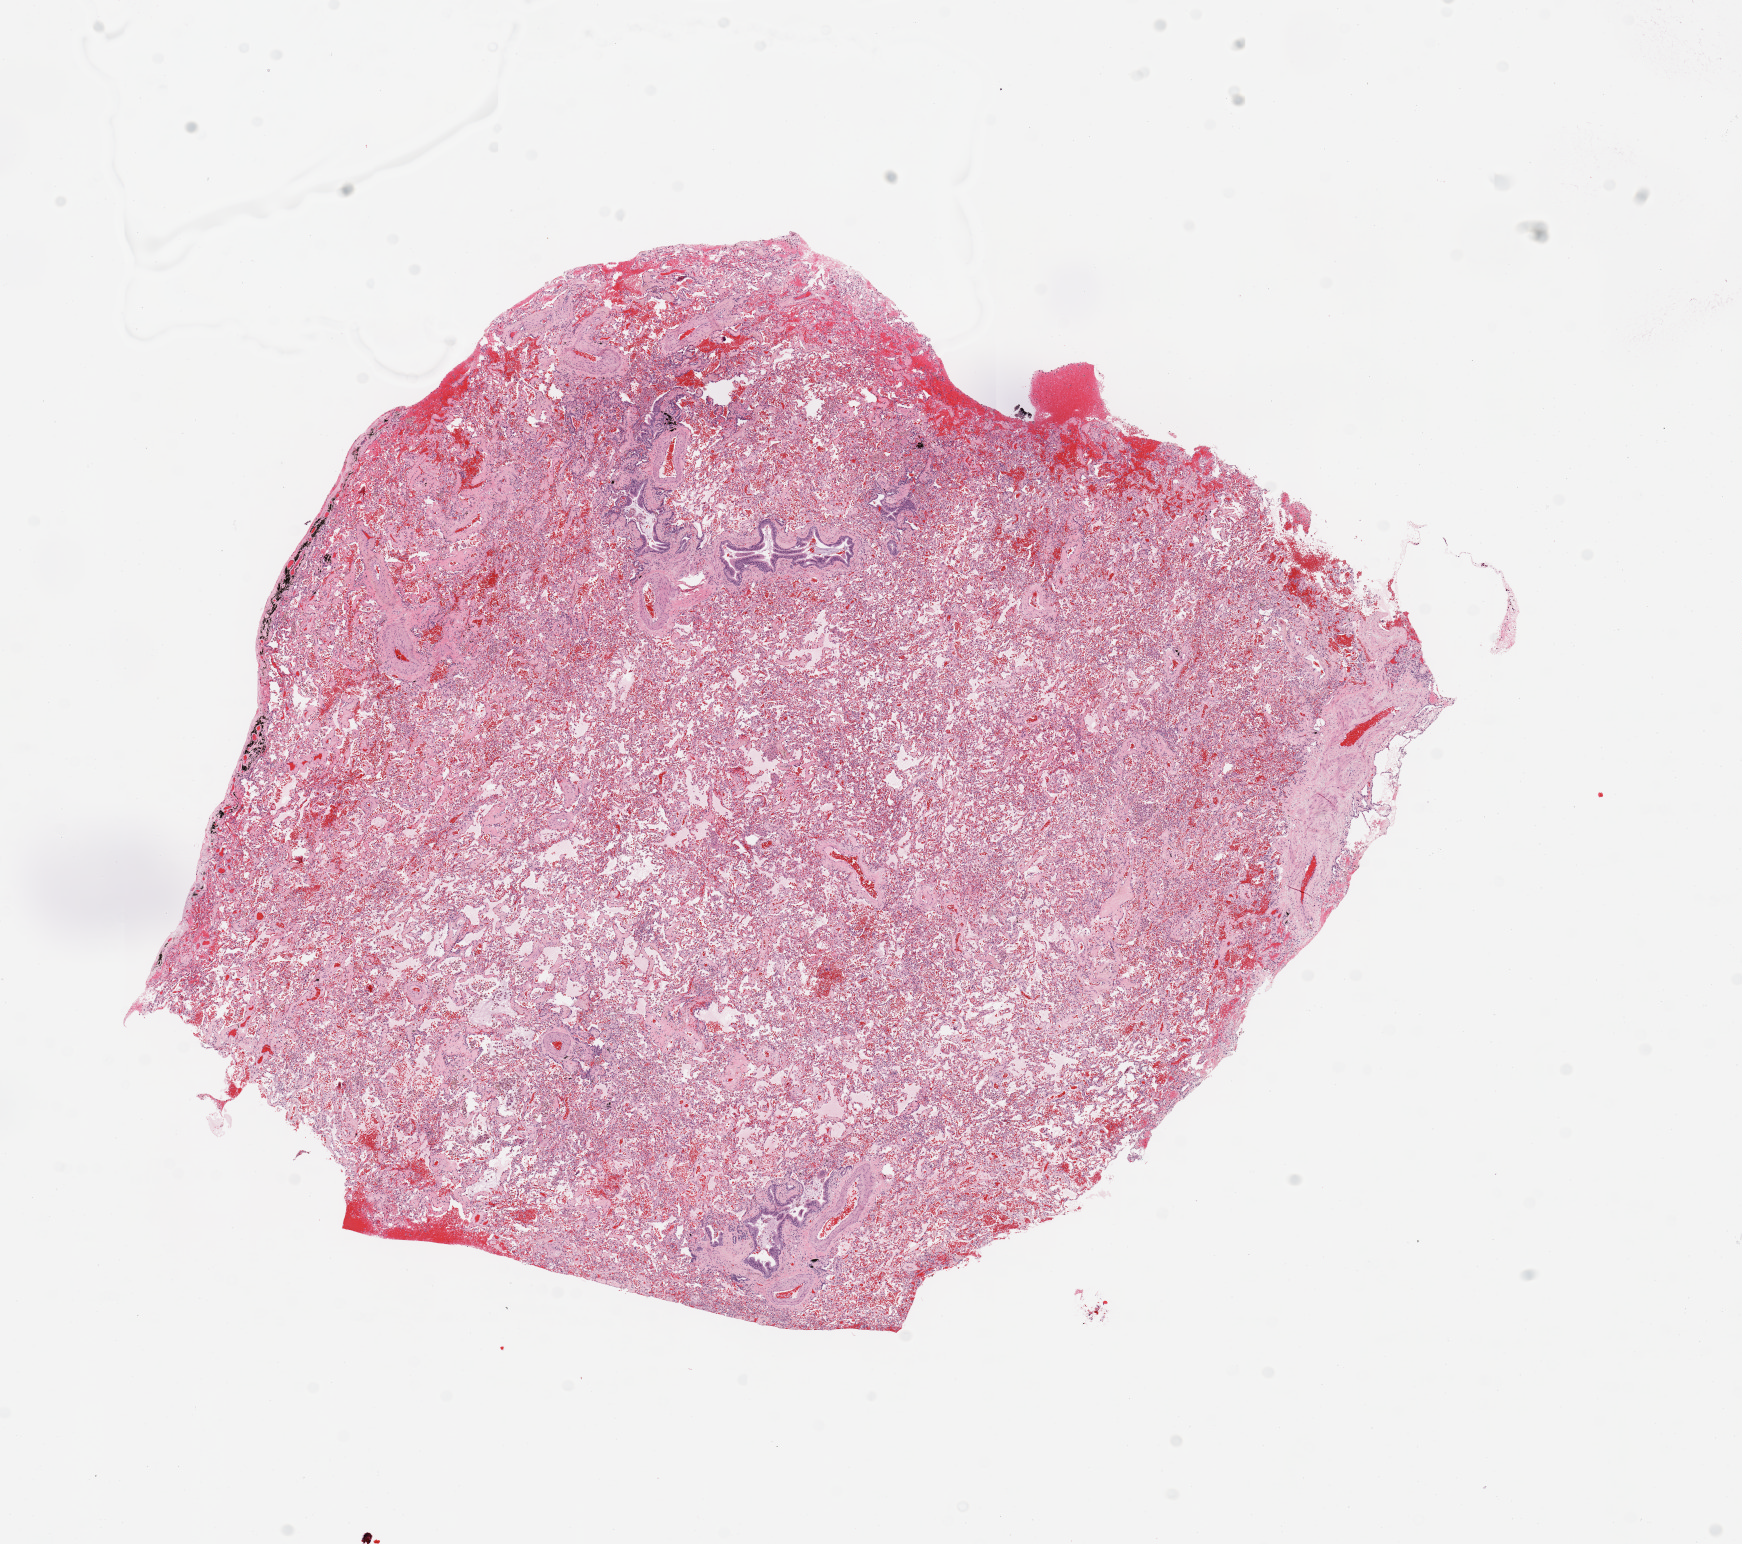
Digitized H&E-stained tissue section (whole slide) — a low-resolution overview of the entire scanned area, about 13.8 x 12.2 mm (from a 20x scan), normal (non-tumour) tissue sample, sampled site: lung. Patient: male, age 62 years.
- this section: normal (non-tumour) tissue from the same patient
- patient diagnosis: Adenocarcinoma, NOS